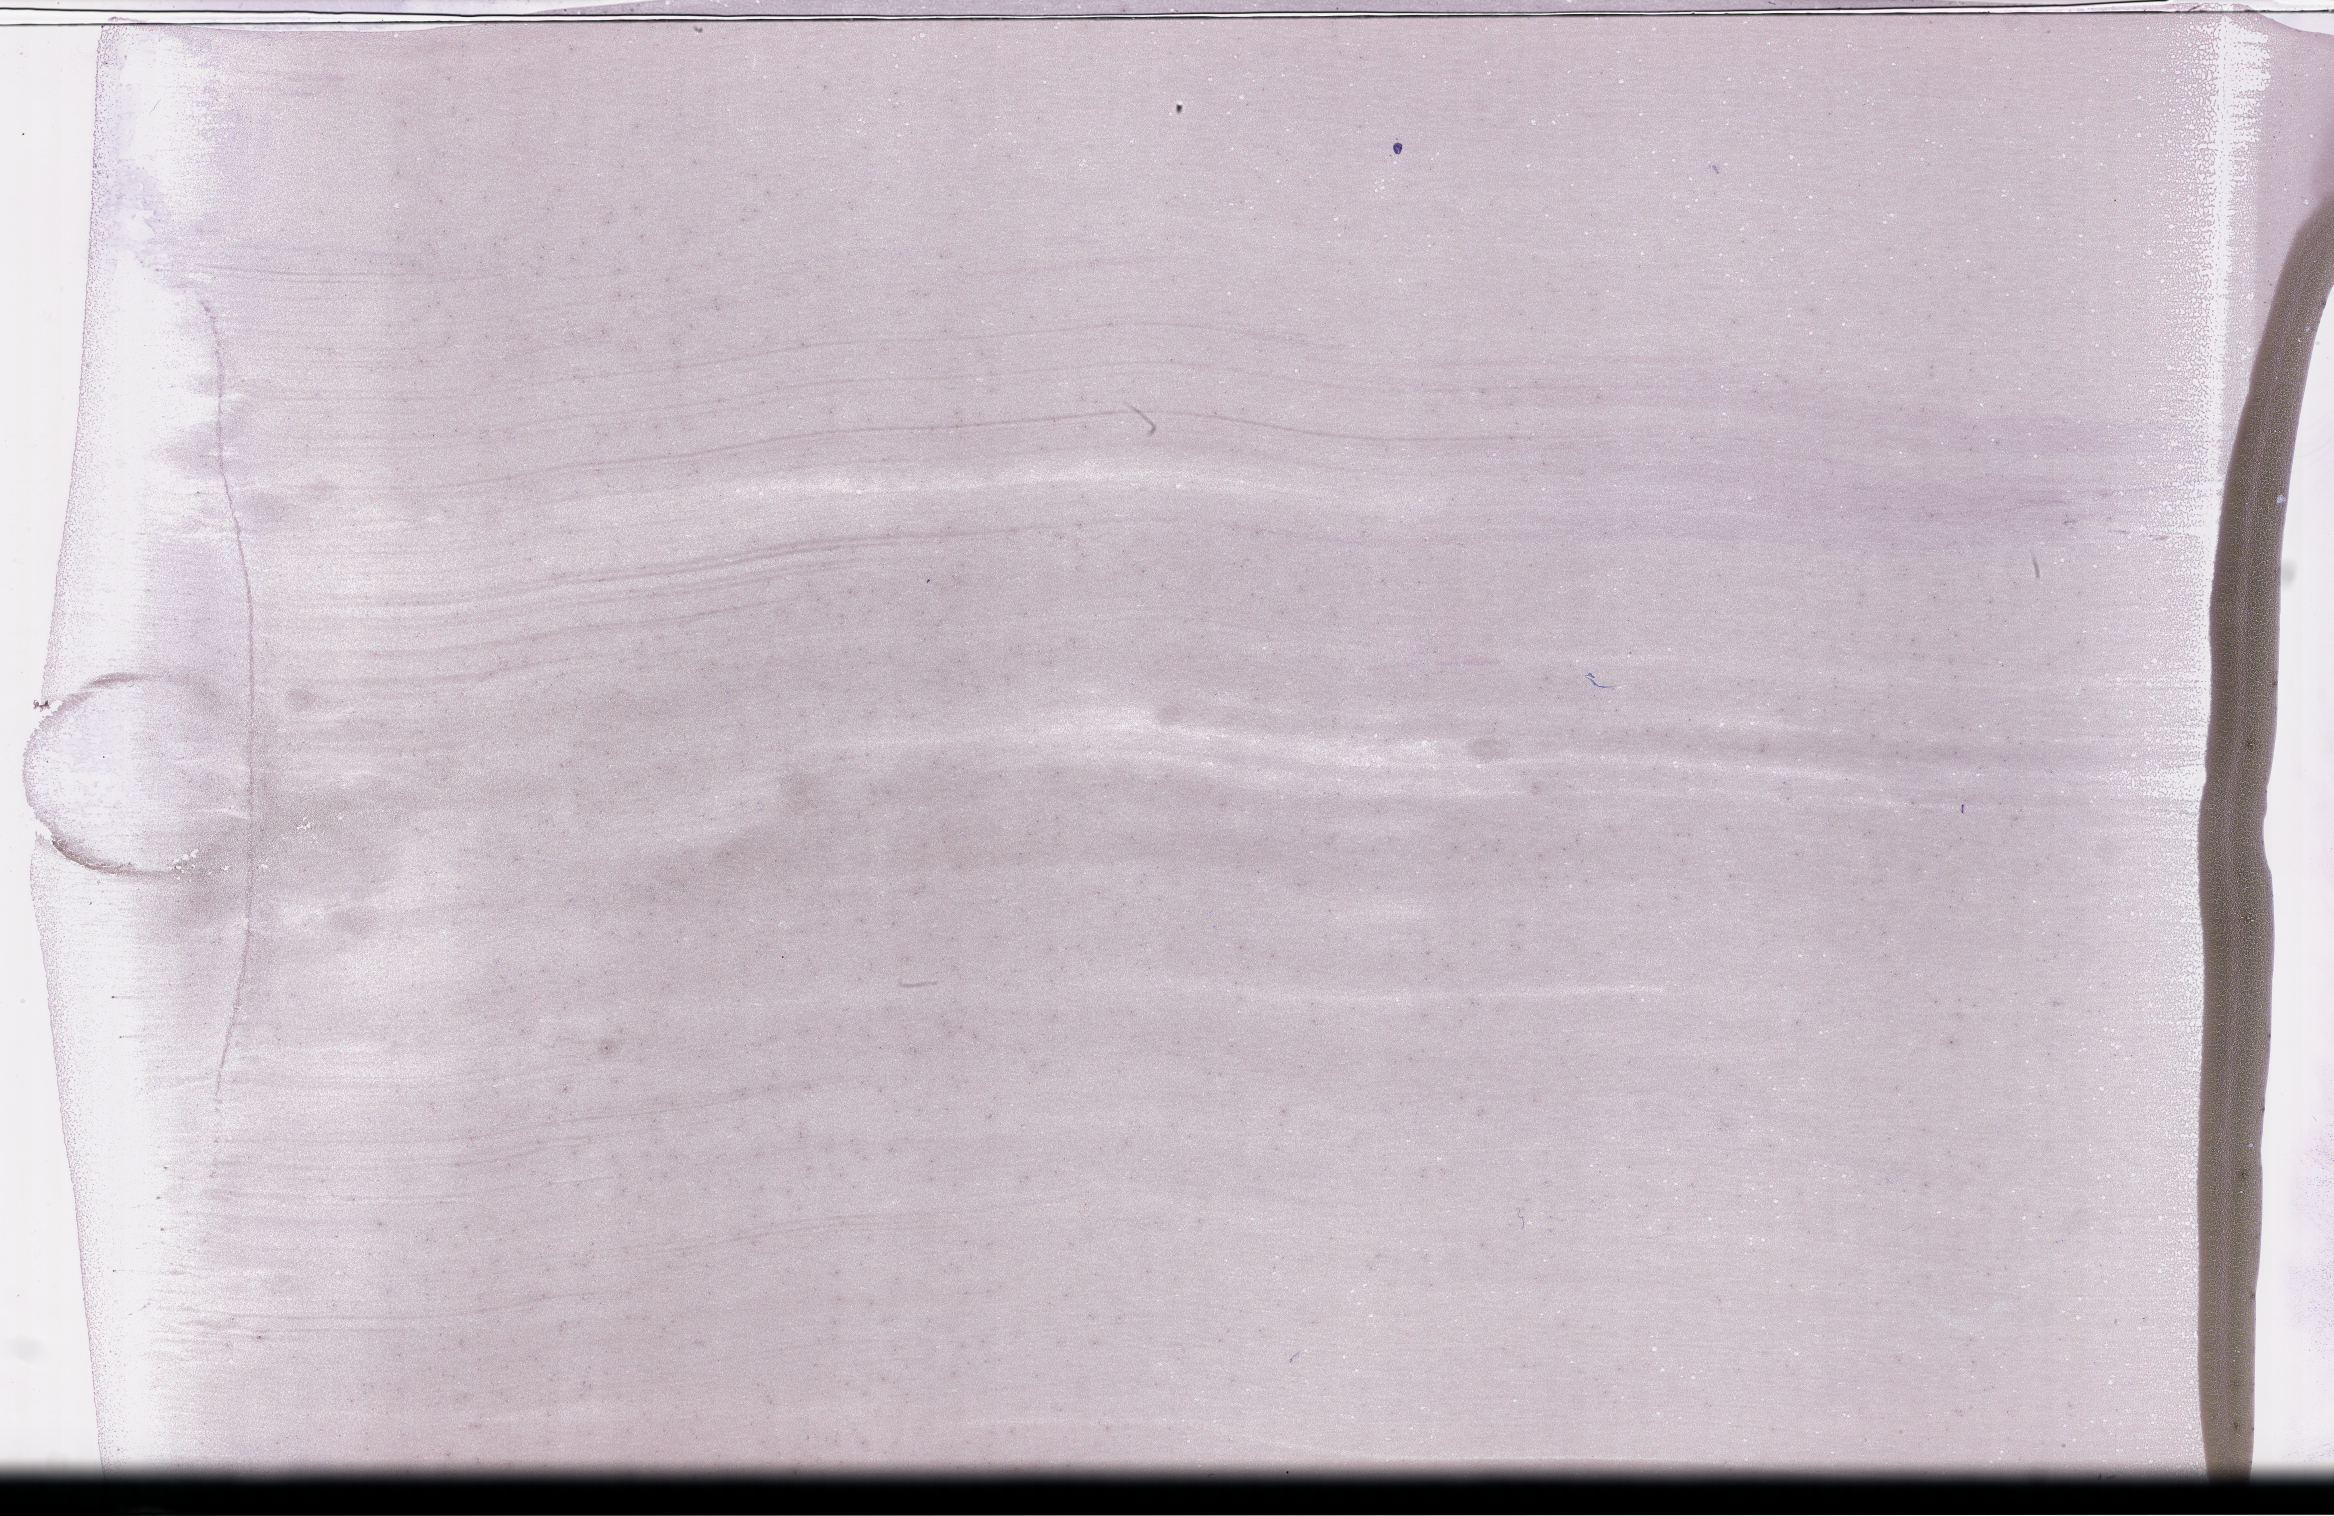
Wright-Giemsa-stained whole blood smear, whole-slide image, shown as a low-resolution overview of the whole scanned area (about 37.7 x 24.5 mm), specimen time point: collected on treatment. Female patient.
From a patient with: Plasma Cell Myeloma.